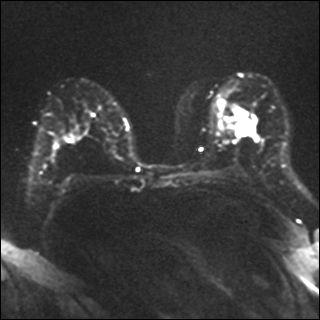
Breast MRI, one axial slice; position 21 of 40 along the scan axis; diffusion-weighted series; image 2 of 4 stored at this slice position (different b-values; order by instance number); 1.5 T; 4 mm slice thickness; 320 × 320 image matrix, field of view 320 × 320 mm. Female patient.
Structures marked on this image (expert manual segmentation):
- tumour on diffusion-weighted imaging: bounding box [x1, y1, x2, y2] px = [229, 105, 252, 134]